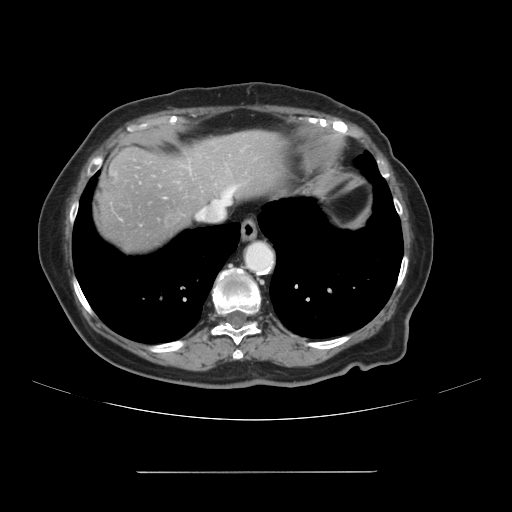
Contrast-enhanced abdominal CT, one axial slice. Slice 97 of 111 in the series (ordered by position). 120 kVp. Soft-tissue window (W 400 / L 40 HU). 512 × 512 image matrix. Female patient, age 74 years. Case-level facts recorded for this patient, not image findings: diagnosis: colorectal cancer liver metastases, imaged before liver resection; multiple liver metastases: yes; largest metastasis: 1.1 cm; disease in both lobes: yes.
Annotated regions visible in this slice (outlined manually by an expert reader):
- hepatic veins: bounding box [x1, y1, x2, y2] px = [214, 191, 231, 207]
- liver: [94, 132, 283, 258]
- planned liver remnant (the part of the liver to remain after resection): [190, 131, 283, 205]
- liver metastasis: [108, 175, 116, 184]
- liver metastasis: [165, 215, 177, 226]